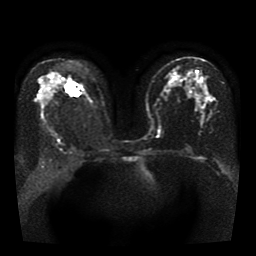
Breast MRI, one axial slice; position 23 of 41 along the scan axis; diffusion-weighted series; image 2 of 4 stored at this slice position (different b-values; order by instance number); 1.5 T; 5 mm slice thickness; 256 × 256 image matrix. Female patient.
Annotated regions visible in this slice (manually delineated by an expert):
- tumour on diffusion-weighted imaging: bounding box (x1, y1, x2, y2) in pixels: (67, 83, 79, 95)